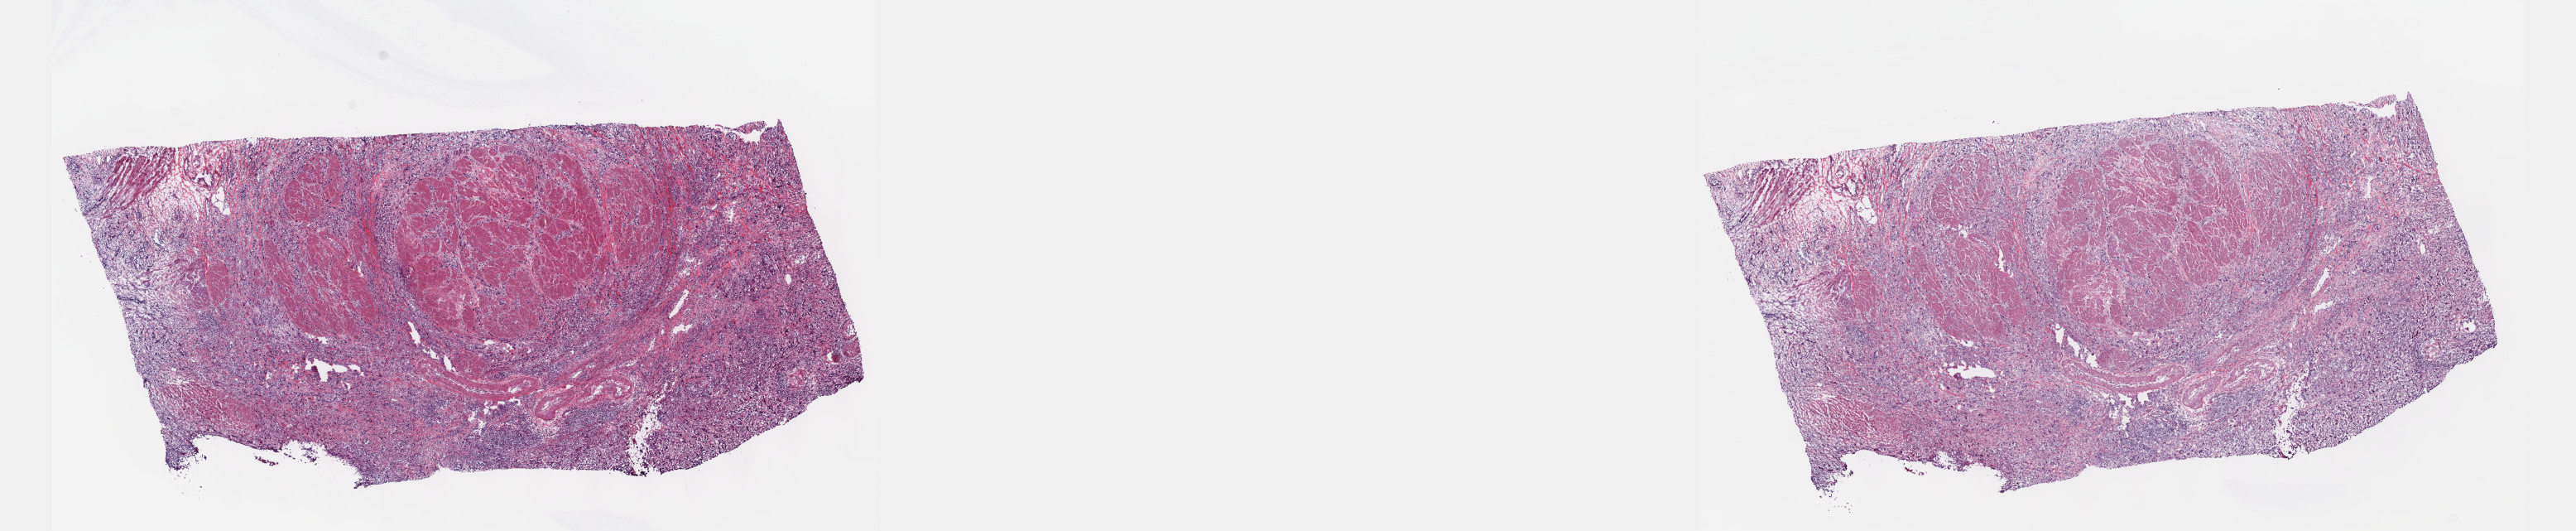
Digitized Hematoxylin and eosin (H&E) stained tissue section (whole slide), shown as a low-resolution overview of the whole scanned area (about 25.1 x 5.2 mm, slide scanned at 40x); frozen section from the top of the tissue portion; primary tumour sample from the bladder. Patient: male, age at initial diagnosis 60 years. Histologic grade: high grade. Slide review estimates, as recorded: tumour cells 75%, tumour nuclei 75%, normal cells 25%, stromal cells 0%, necrosis 0%. Inflammatory infiltration, as recorded: lymphocyte infiltration 4%, monocyte infiltration 0%, neutrophil infiltration 0%.
AJCC pathologic stage: III (7th edition). Diagnosis: Transitional cell carcinoma.